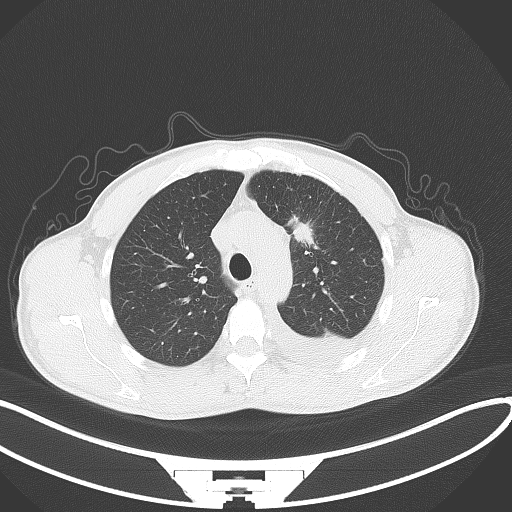
Chest CT, one axial slice; position 96 of 130 along the scan axis; reconstruction kernel B70f; 120 kVp; lung window (W 1500 / L -600 HU); 3 mm slice thickness; 512 × 512 image matrix, field of view 400 × 400 mm. Patient: male, 49 years. Case-level facts recorded for this patient, not image findings: clinical TNM (as recorded): T1c N1 M1.
Structures marked on this image (rectangle marked by the reading radiologist):
- lung tumour (recorded histology: adenocarcinoma): bounding box [x1, y1, x2, y2] px = [290, 211, 319, 256]